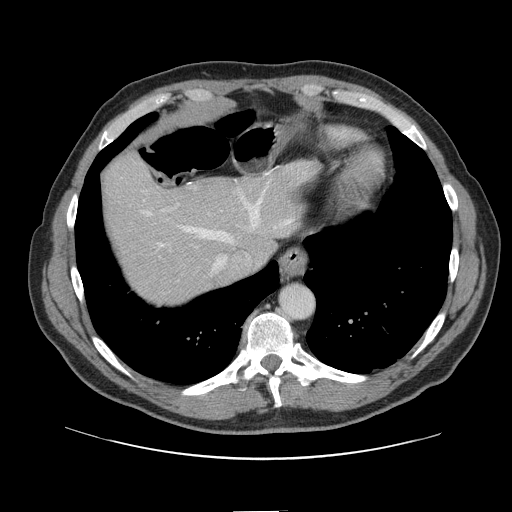
Contrast-enhanced abdominal CT, one axial slice; position 123 of 161 along the scan axis; 120 kVp; intravenous contrast given; soft-tissue window (W 400 / L 40 HU); 2.5 mm slice thickness; 512 × 512 image matrix, field of view 412 × 412 mm. Male patient, age 66 years. Case-level facts recorded for this patient, not image findings: diagnosis: colorectal cancer liver metastases, imaged before liver resection; multiple liver metastases: no; largest metastasis: 3.5 cm; disease in both lobes: no.
Annotated regions visible in this slice (manually delineated by an expert):
- hepatic veins: bounding box (x1, y1, x2, y2) in pixels: (143, 183, 293, 275)
- liver: (103, 155, 311, 304)
- planned liver remnant (the part of the liver to remain after resection): (103, 155, 311, 295)